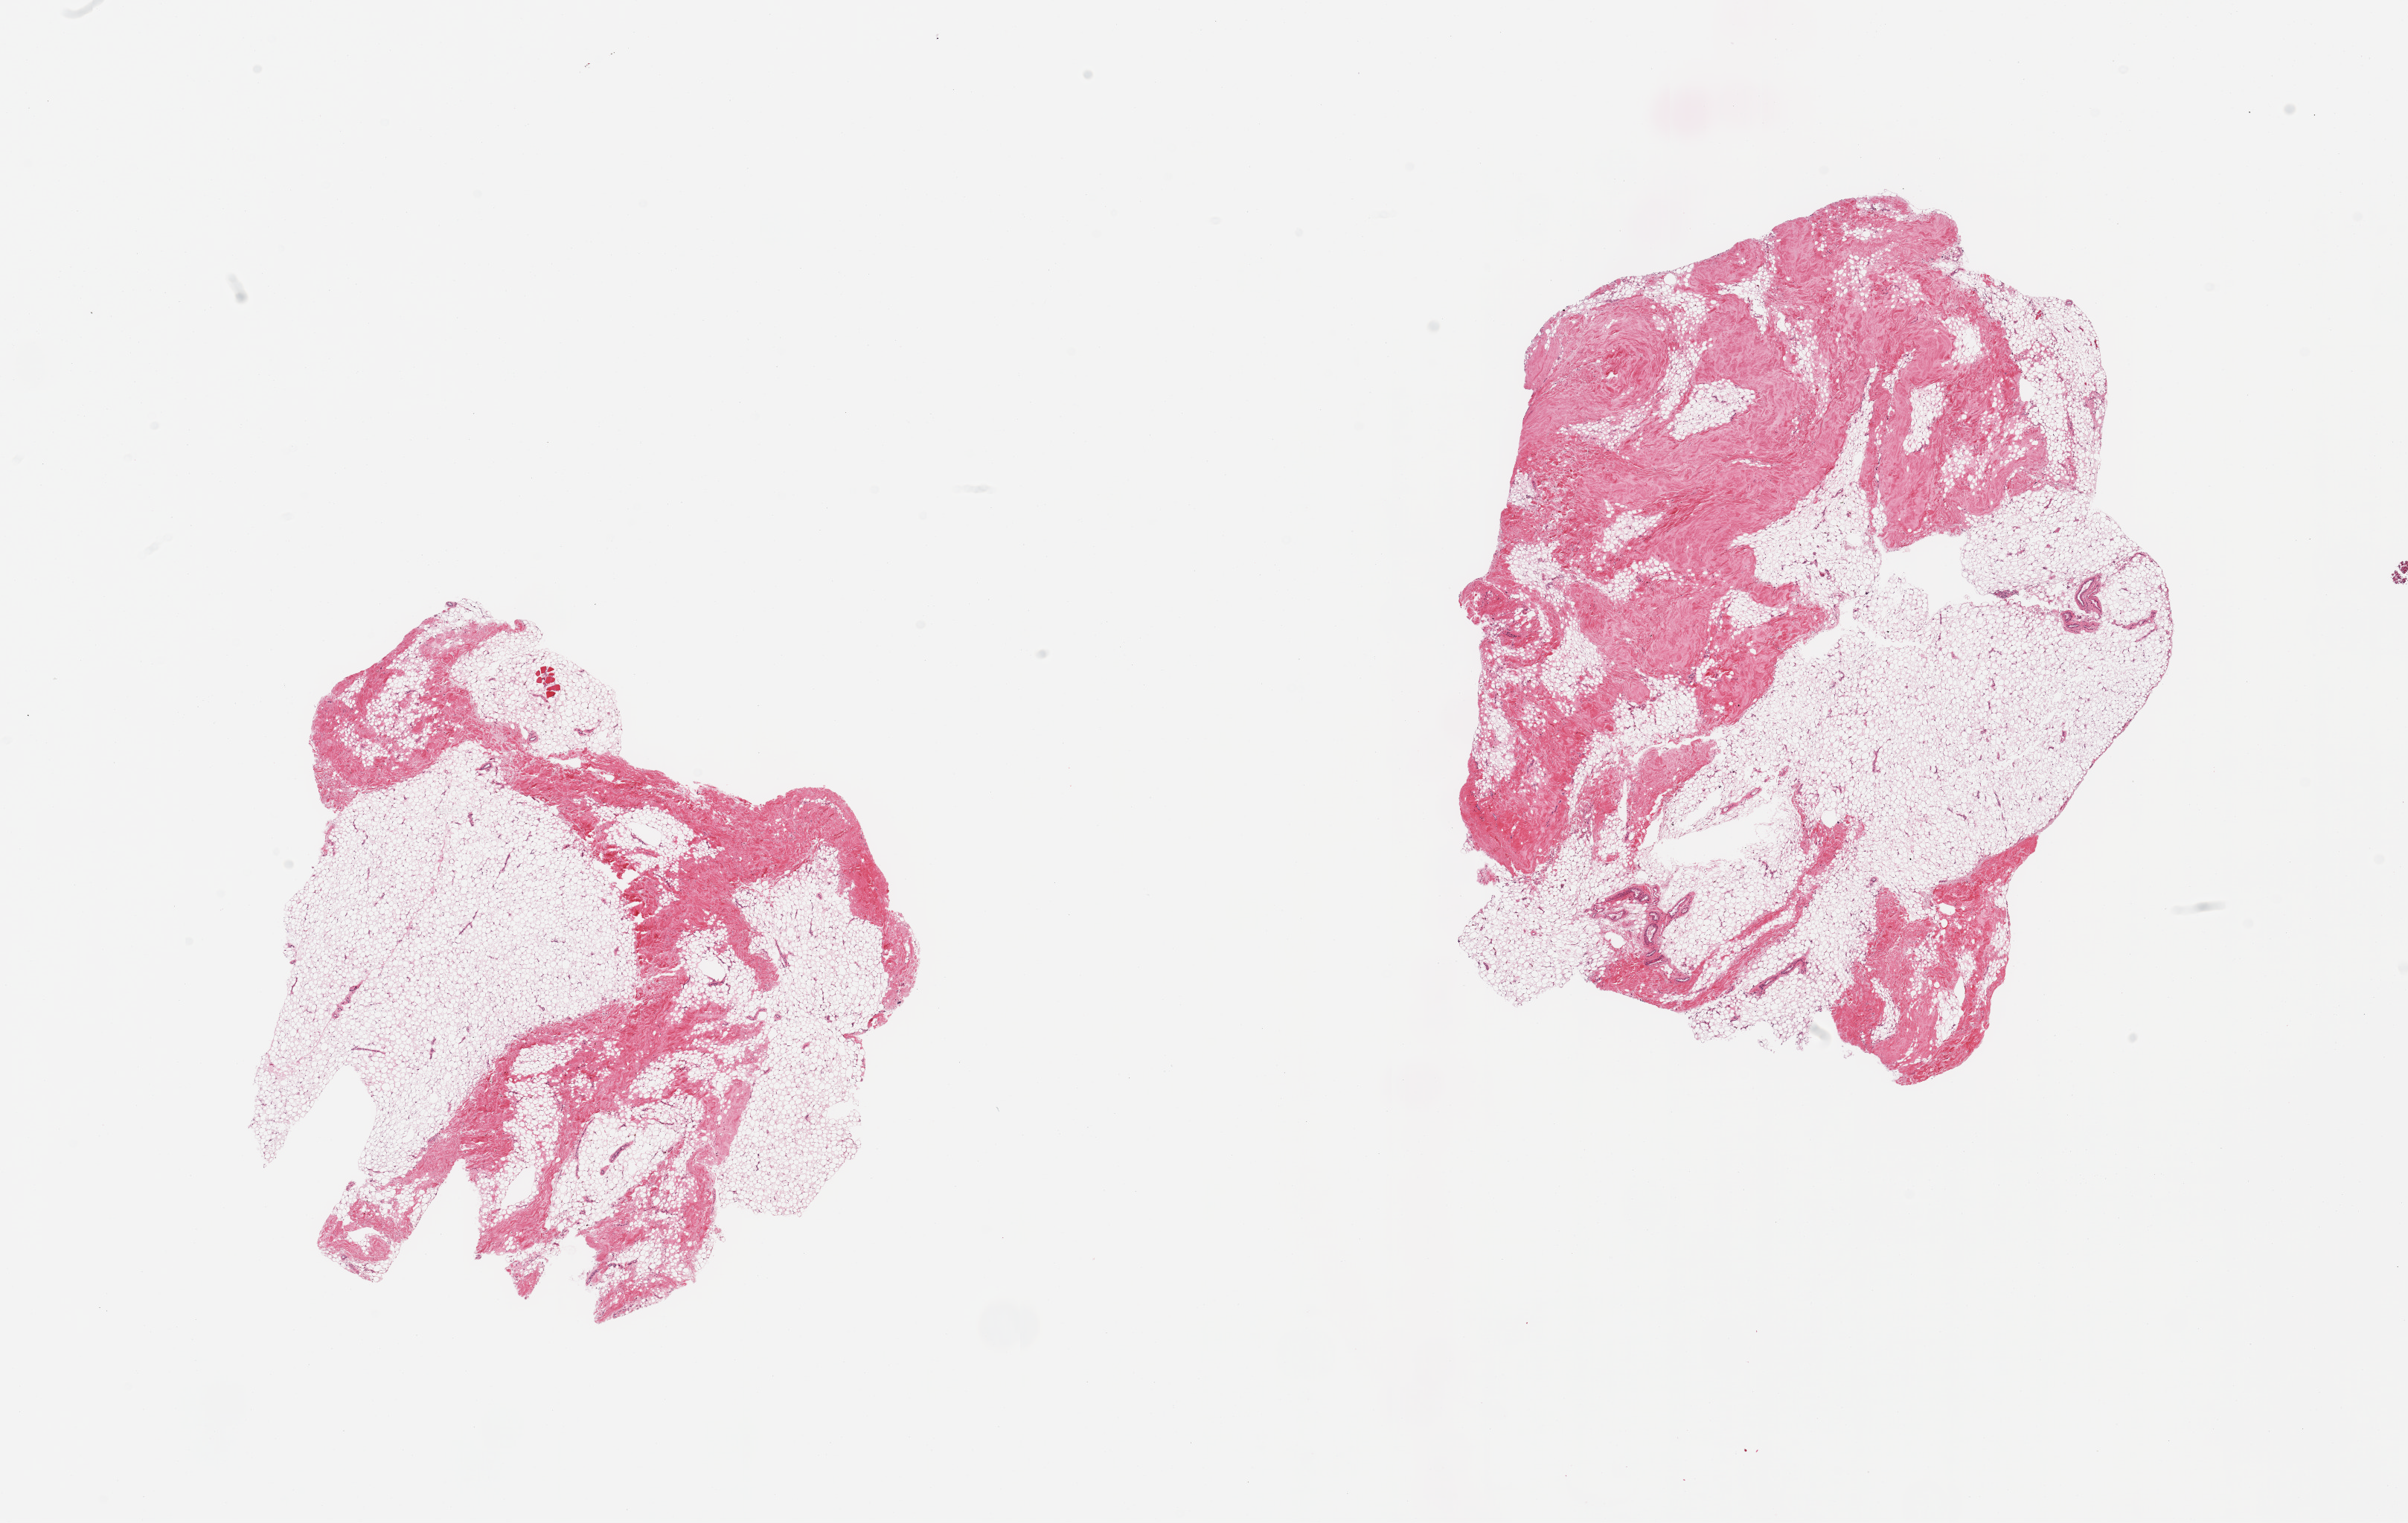
H&E whole-slide image, brightfield, shown as a low-resolution overview of the whole scanned area (about 25.6 x 16.2 mm), PAXgene-fixed, paraffin-embedded tissue, sampled site (target tissue): breast, tissue donor sample. Donor sex: male.
Pathologist's review note for this sample: 2 pieces; fat with 30 and 50% fibrous tissue, rare skeletal muscle fibers.